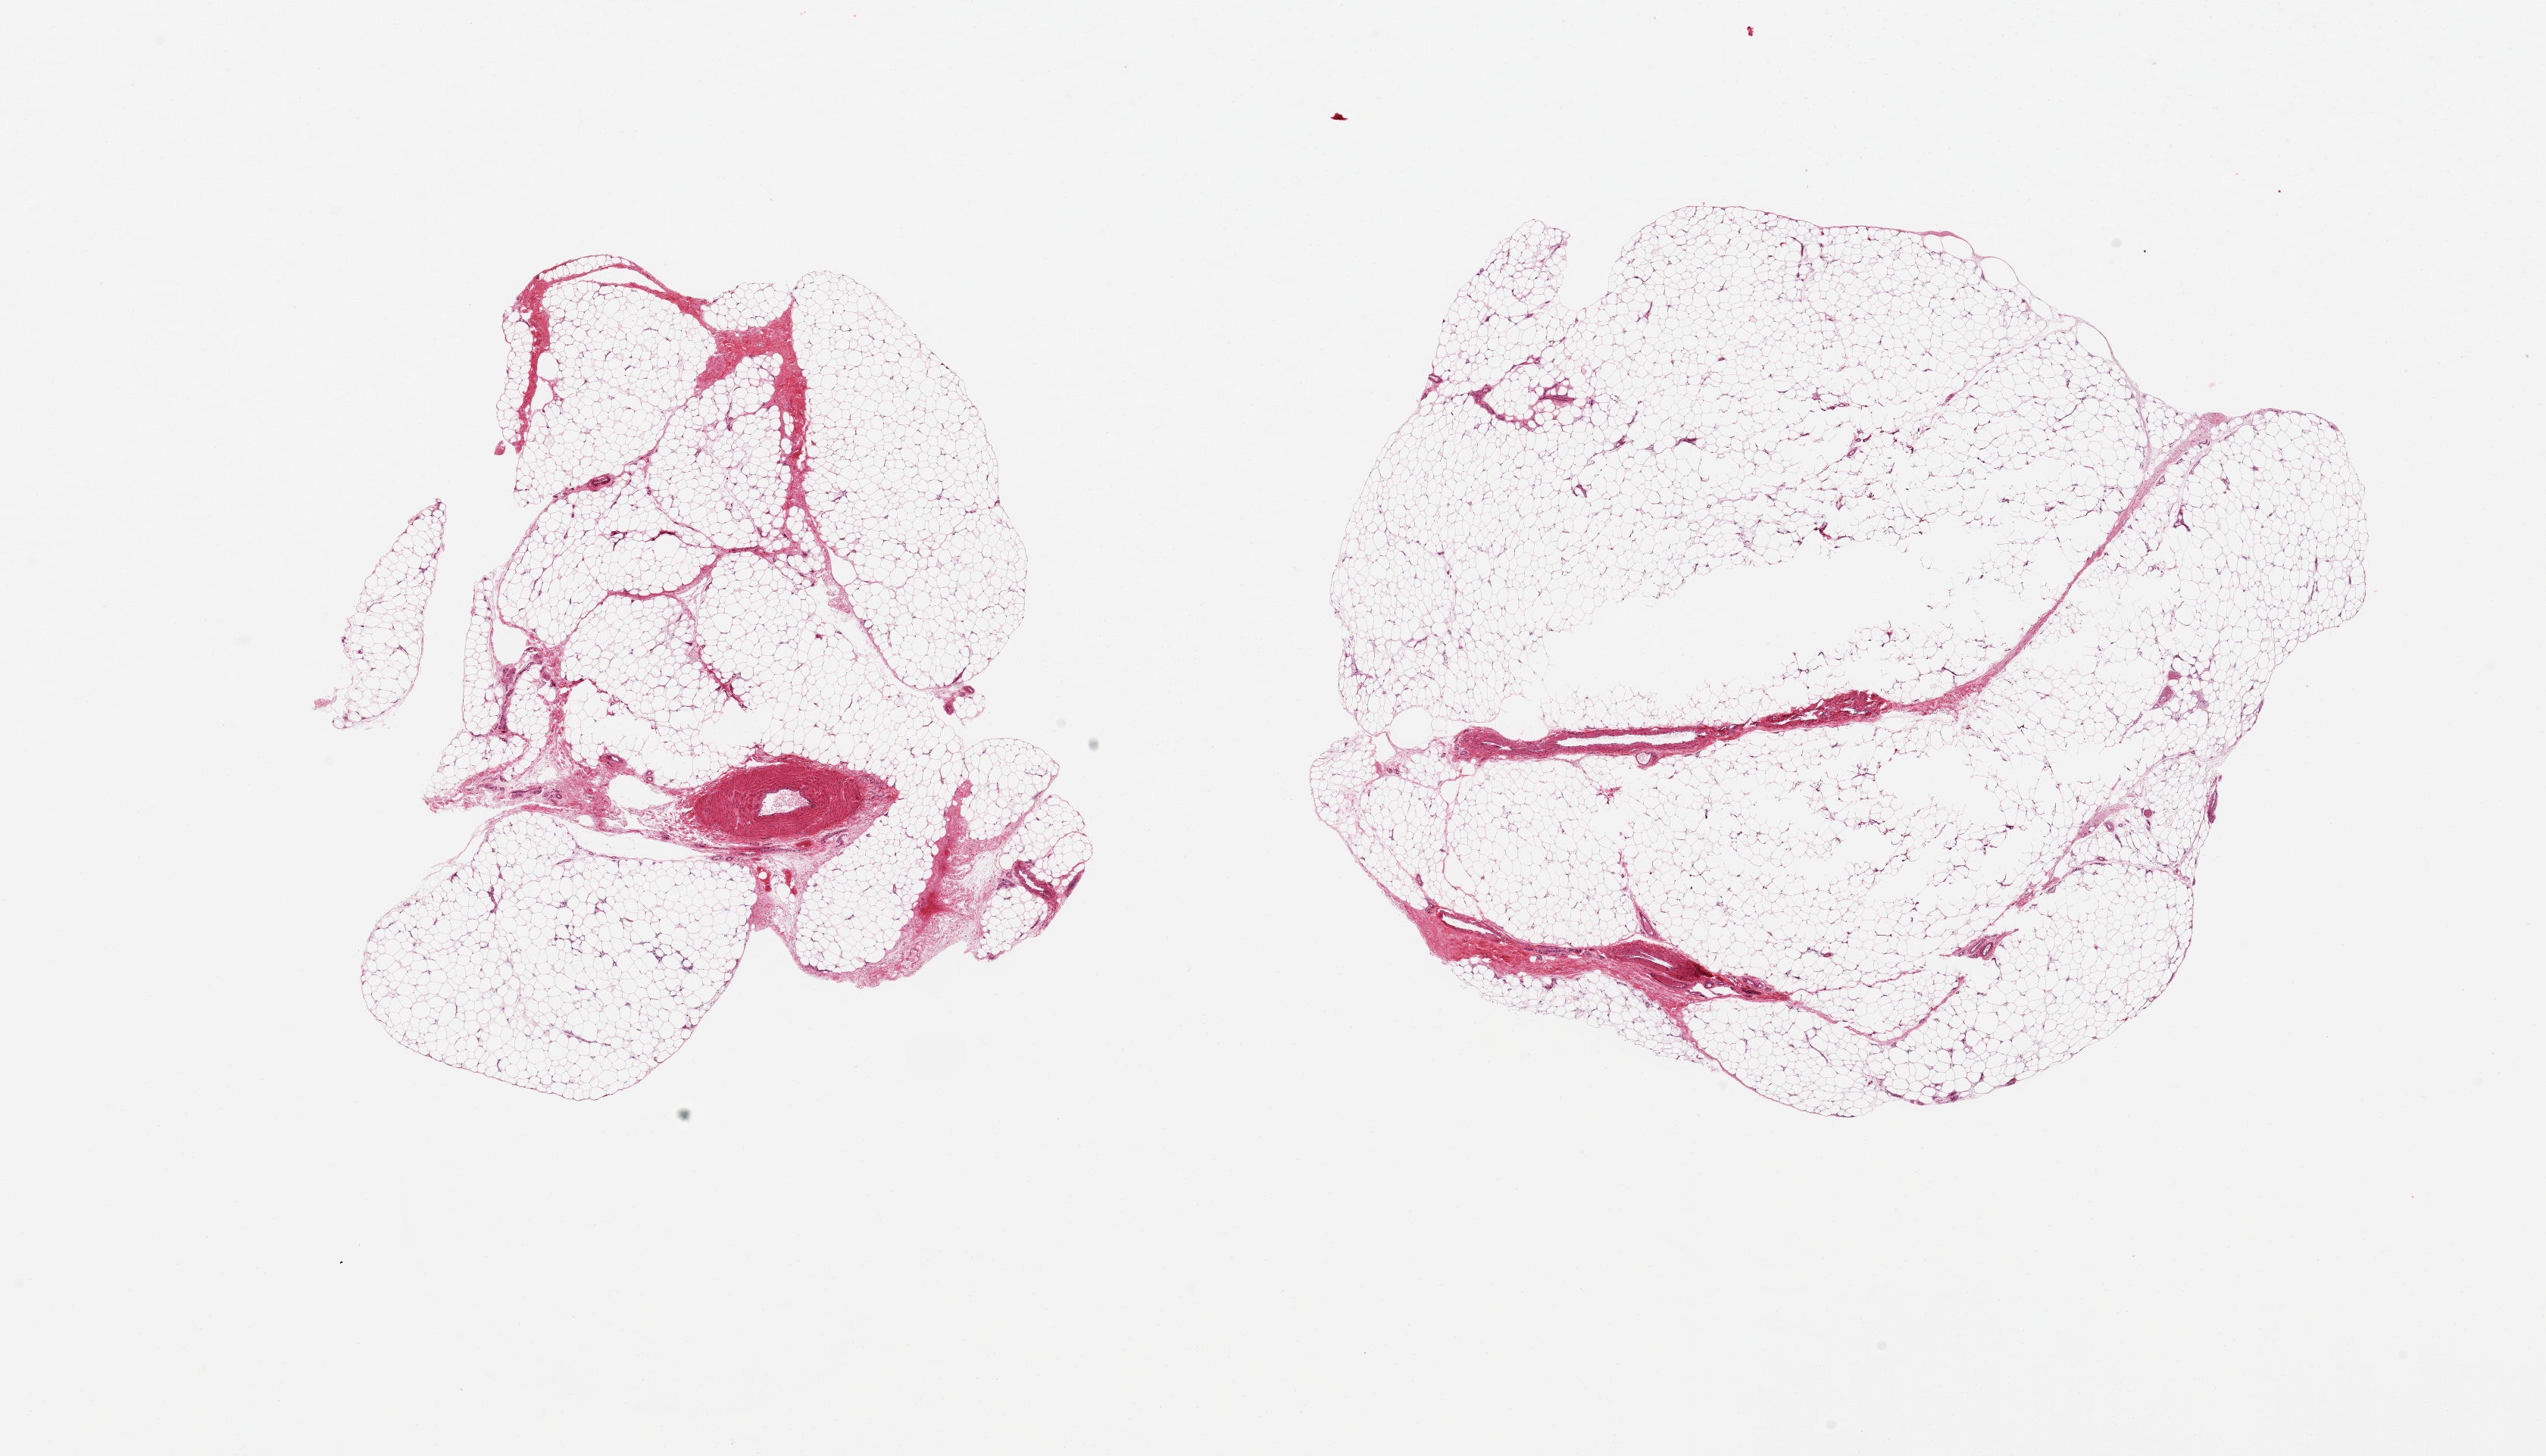
Whole-slide image, H&E stain, shown as a low-resolution overview of the whole scanned area (about 26.6 x 15.2 mm); PAXgene-fixed paraffin-embedded (PFPE) section; target tissue: adipose tissue; donor tissue sample. Female donor.
* reviewer comment on this tissue sample: 2 pieces, ~8x8mm. One with focal central under-fixation